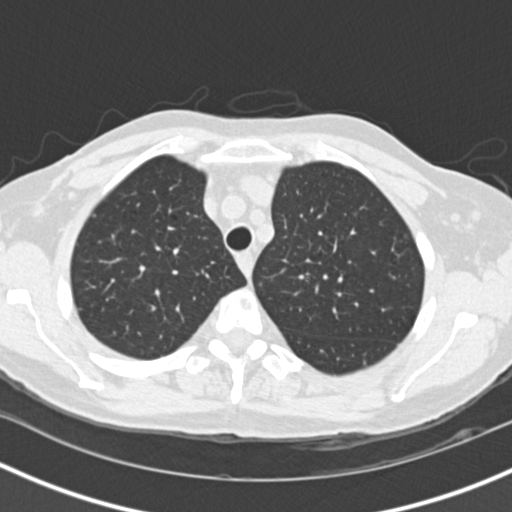
Low-dose screening chest CT, axial slice. First (baseline) screen. Lung window (W 1500 / L -600 HU). 2 mm slice thickness. Standard (soft-tissue) reconstruction kernel (B30f). Slice 31 of 146 in the series. Female, age 73 years at enrolment. Current smoker at enrolment.
• Expert-annotated lung lesion, bounding box <317,205,374,274> (left, top, right, bottom; pixels).
• Reader record for this screening exam (exam-level; its link to the box is not recorded): non-calcified nodule or mass ≥4 mm, left upper lobe, 27 × 21 mm, spiculated (stellate) margins, soft tissue attenuation.
• Official screen result: positive, change unspecified: nodule(s) >= 4 mm or enlarging nodule(s), mass(es), or other non-specific abnormalities suspicious for lung cancer.
• Participant outcome: lung cancer diagnosed 72 days after this screen — bronchiolo-alveolar adenocarcinoma, NOS, left upper lobe, moderately differentiated (G2), stage IIIB (AJCC 6th edition), 17 mm at pathology.